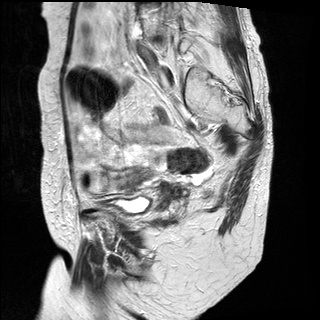
Pelvic MRI for cervical cancer, one sagittal slice. Position 9 of 31 along the scan axis. T2-weighted. 1.5 T. TE 89 ms, TR 3890 ms. 320 × 320 image matrix, field of view 260 × 260 mm. Female patient, age 61 years.
Annotated regions visible in this slice (expert manual segmentation):
- uterus and cervix: bounding box <153,180,190,214> (left, top, right, bottom; pixels)